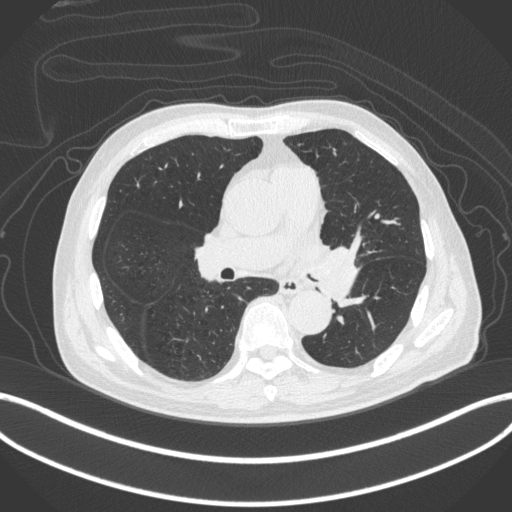
Chest CT, one axial slice; slice 234 of 420 in the series (ordered by position); 120 kVp; lung window (W 1500 / L -600 HU); 512 × 512 image matrix, field of view 400 × 400 mm. Male patient, age 77 years. Case-level facts recorded for this patient, not image findings: clinical TNM (as recorded): T3 N1 M0.
Structures marked on this image (bounding box drawn by a radiologist):
- lung tumour (recorded histology: adenocarcinoma): bounding box <310,240,361,305> (left, top, right, bottom; pixels)